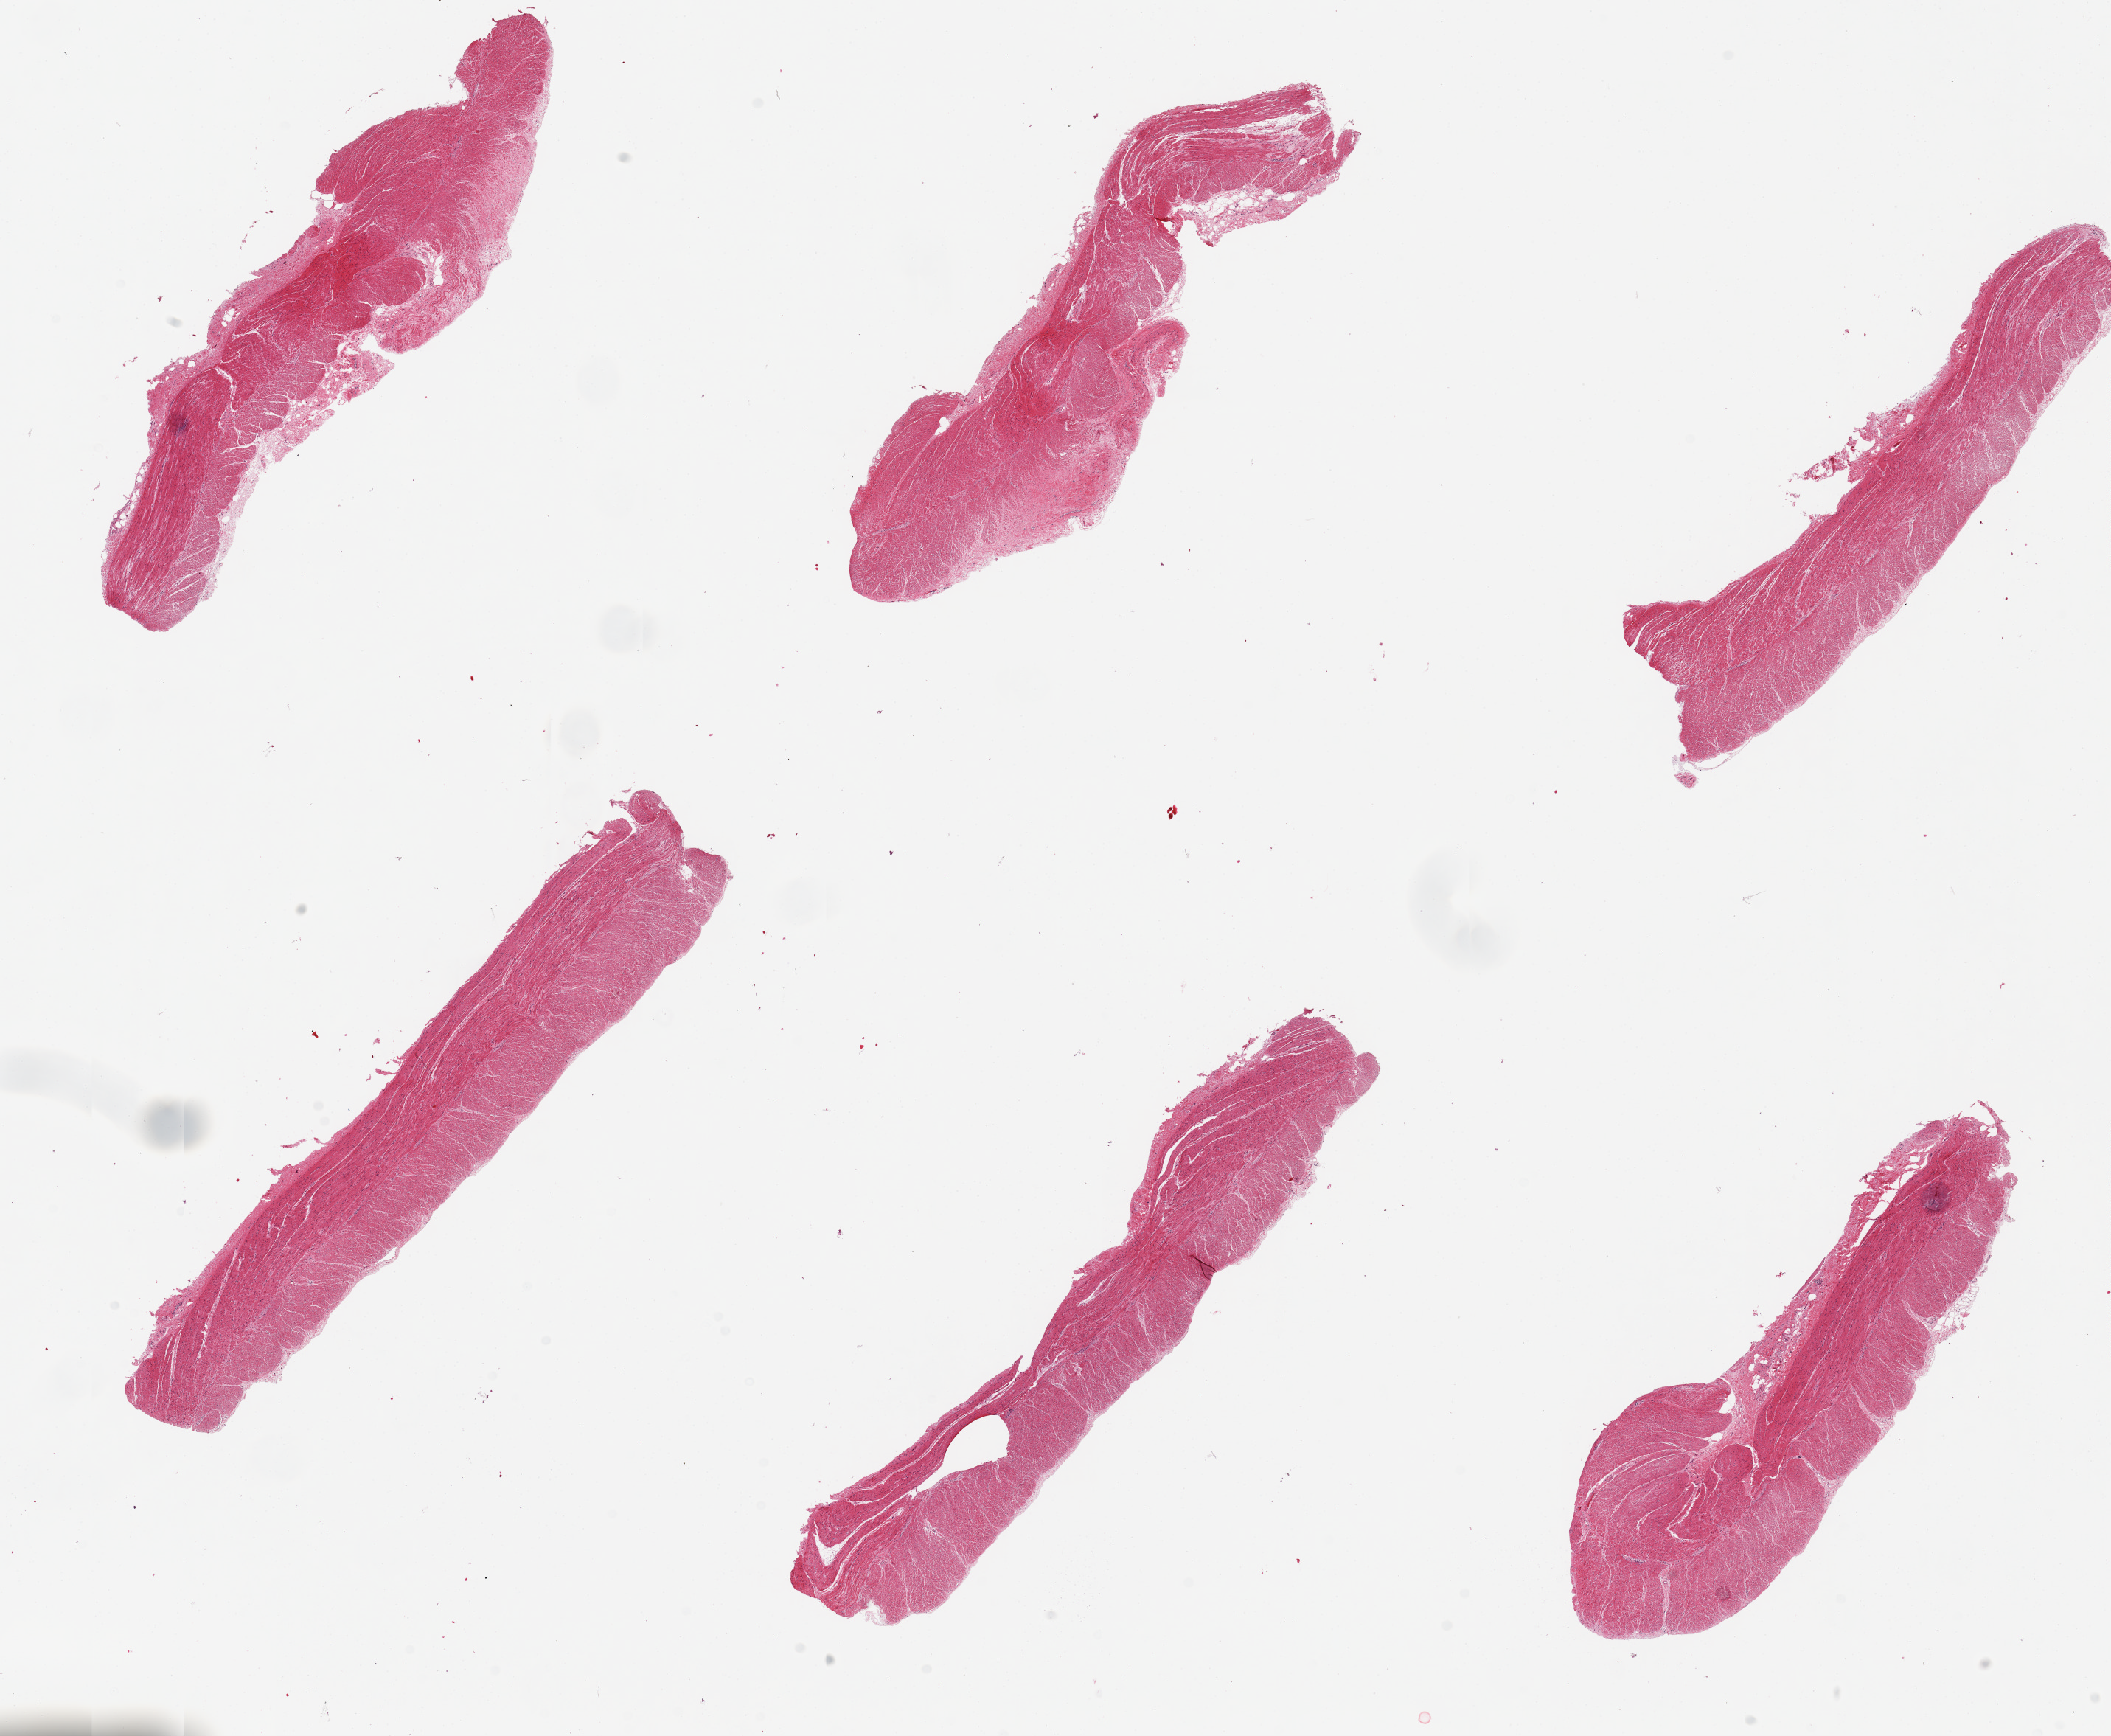
Digitized haematoxylin and eosin-stained section, a low-resolution overview of the entire scanned area, about 22.6 x 18.6 mm. PAXgene-fixed, paraffin-embedded tissue. Sampled site (target tissue): sigmoid colon. Tissue donor sample. Male donor.
Pathologist's review note for this sample: 6 pieces, all muscularis, good specimens.